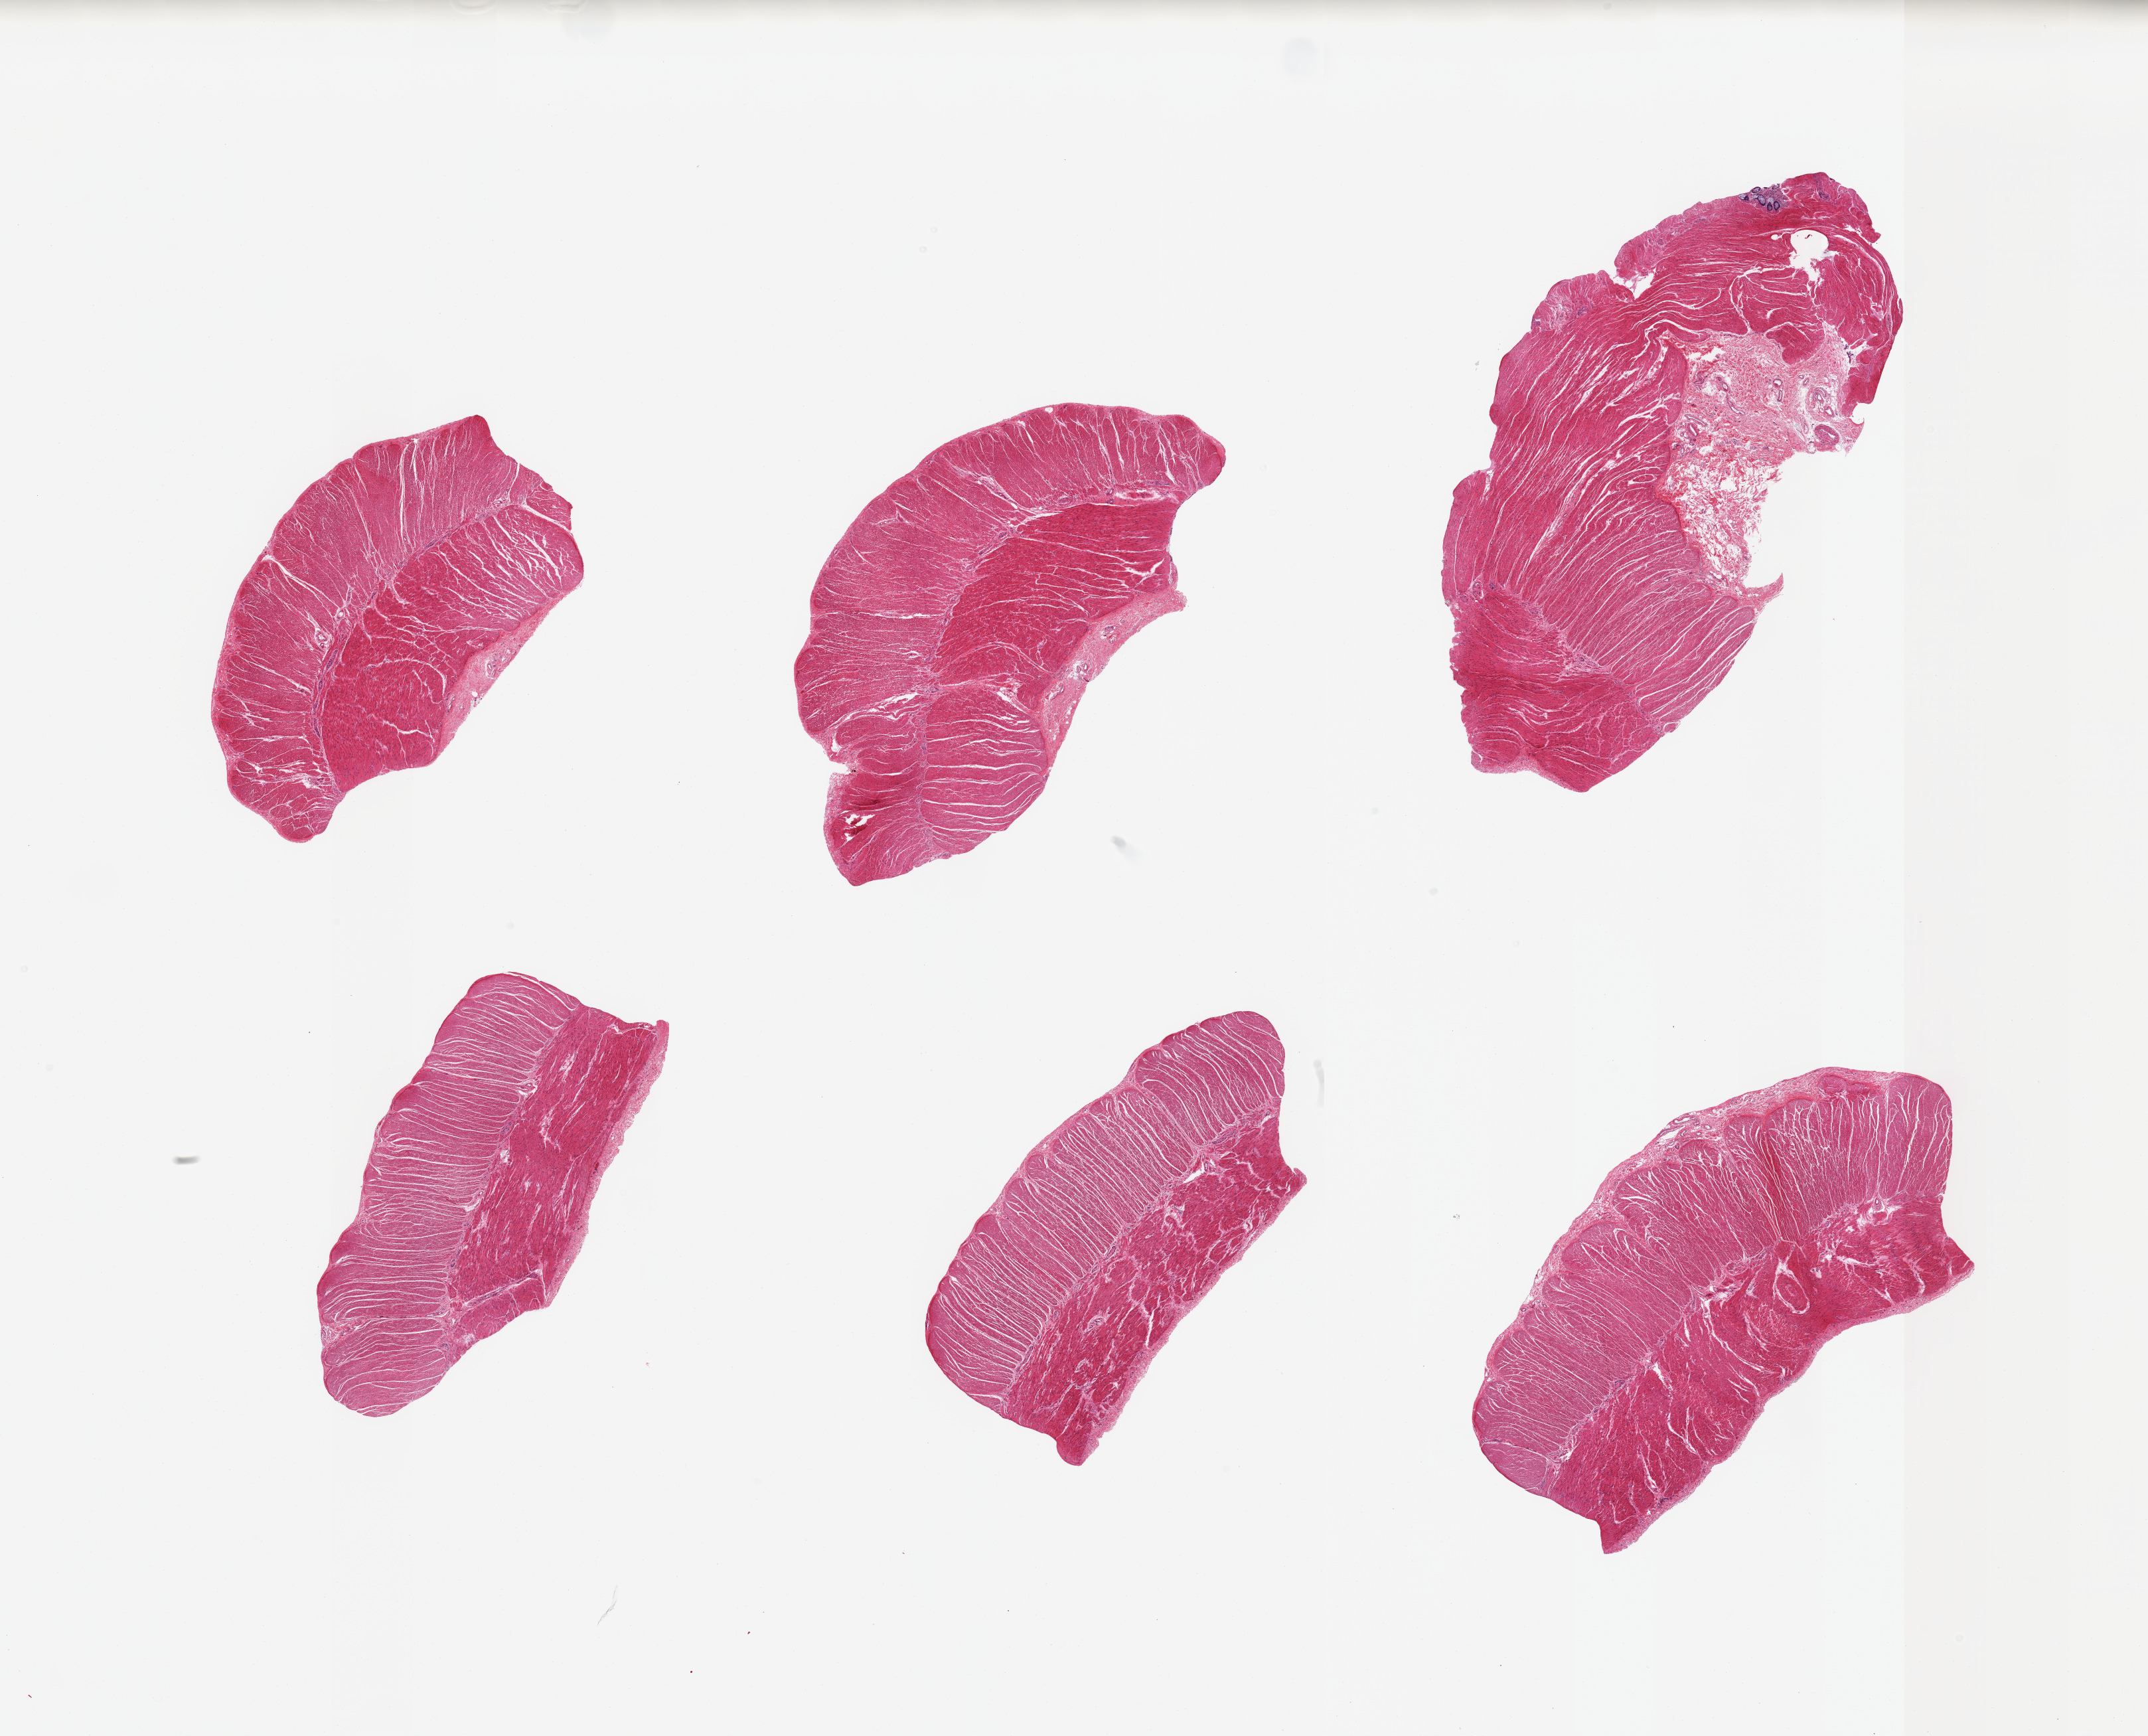
Digitized hematoxylin and eosin (H&E)-stained section, a low-resolution overview of the entire scanned area, about 25.6 x 20.7 mm. PAXgene-fixed paraffin-embedded (PFPE) section. Section of sigmoid colon (target tissue). Tissue donor sample. Donor sex: female.
• pathologist's review note for this sample: 6 pieces, confirmed target muscularis